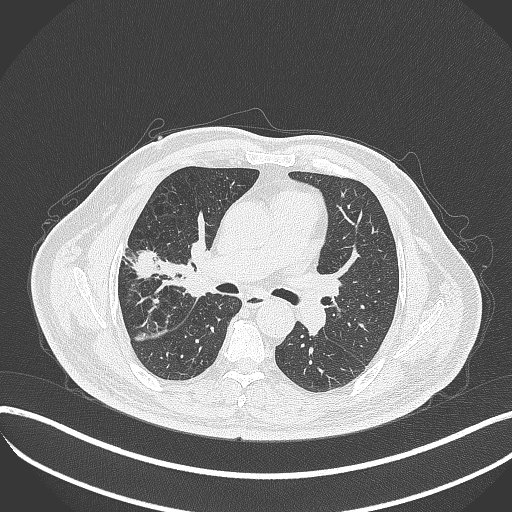
Chest CT, one axial slice; position 210 of 401 along the scan axis; reconstruction kernel B70f; 120 kVp; lung window (W 1500 / L -600 HU); 512 × 512 image matrix. Male patient, age 72 years. From the clinical record (not read from this slice): clinical TNM (as recorded): T1c N0 M0.
Structures marked on this image (bounding box drawn by a radiologist):
- lung tumour (recorded histology: squamous cell carcinoma): box from (x=159, y=243) to (x=219, y=303) px